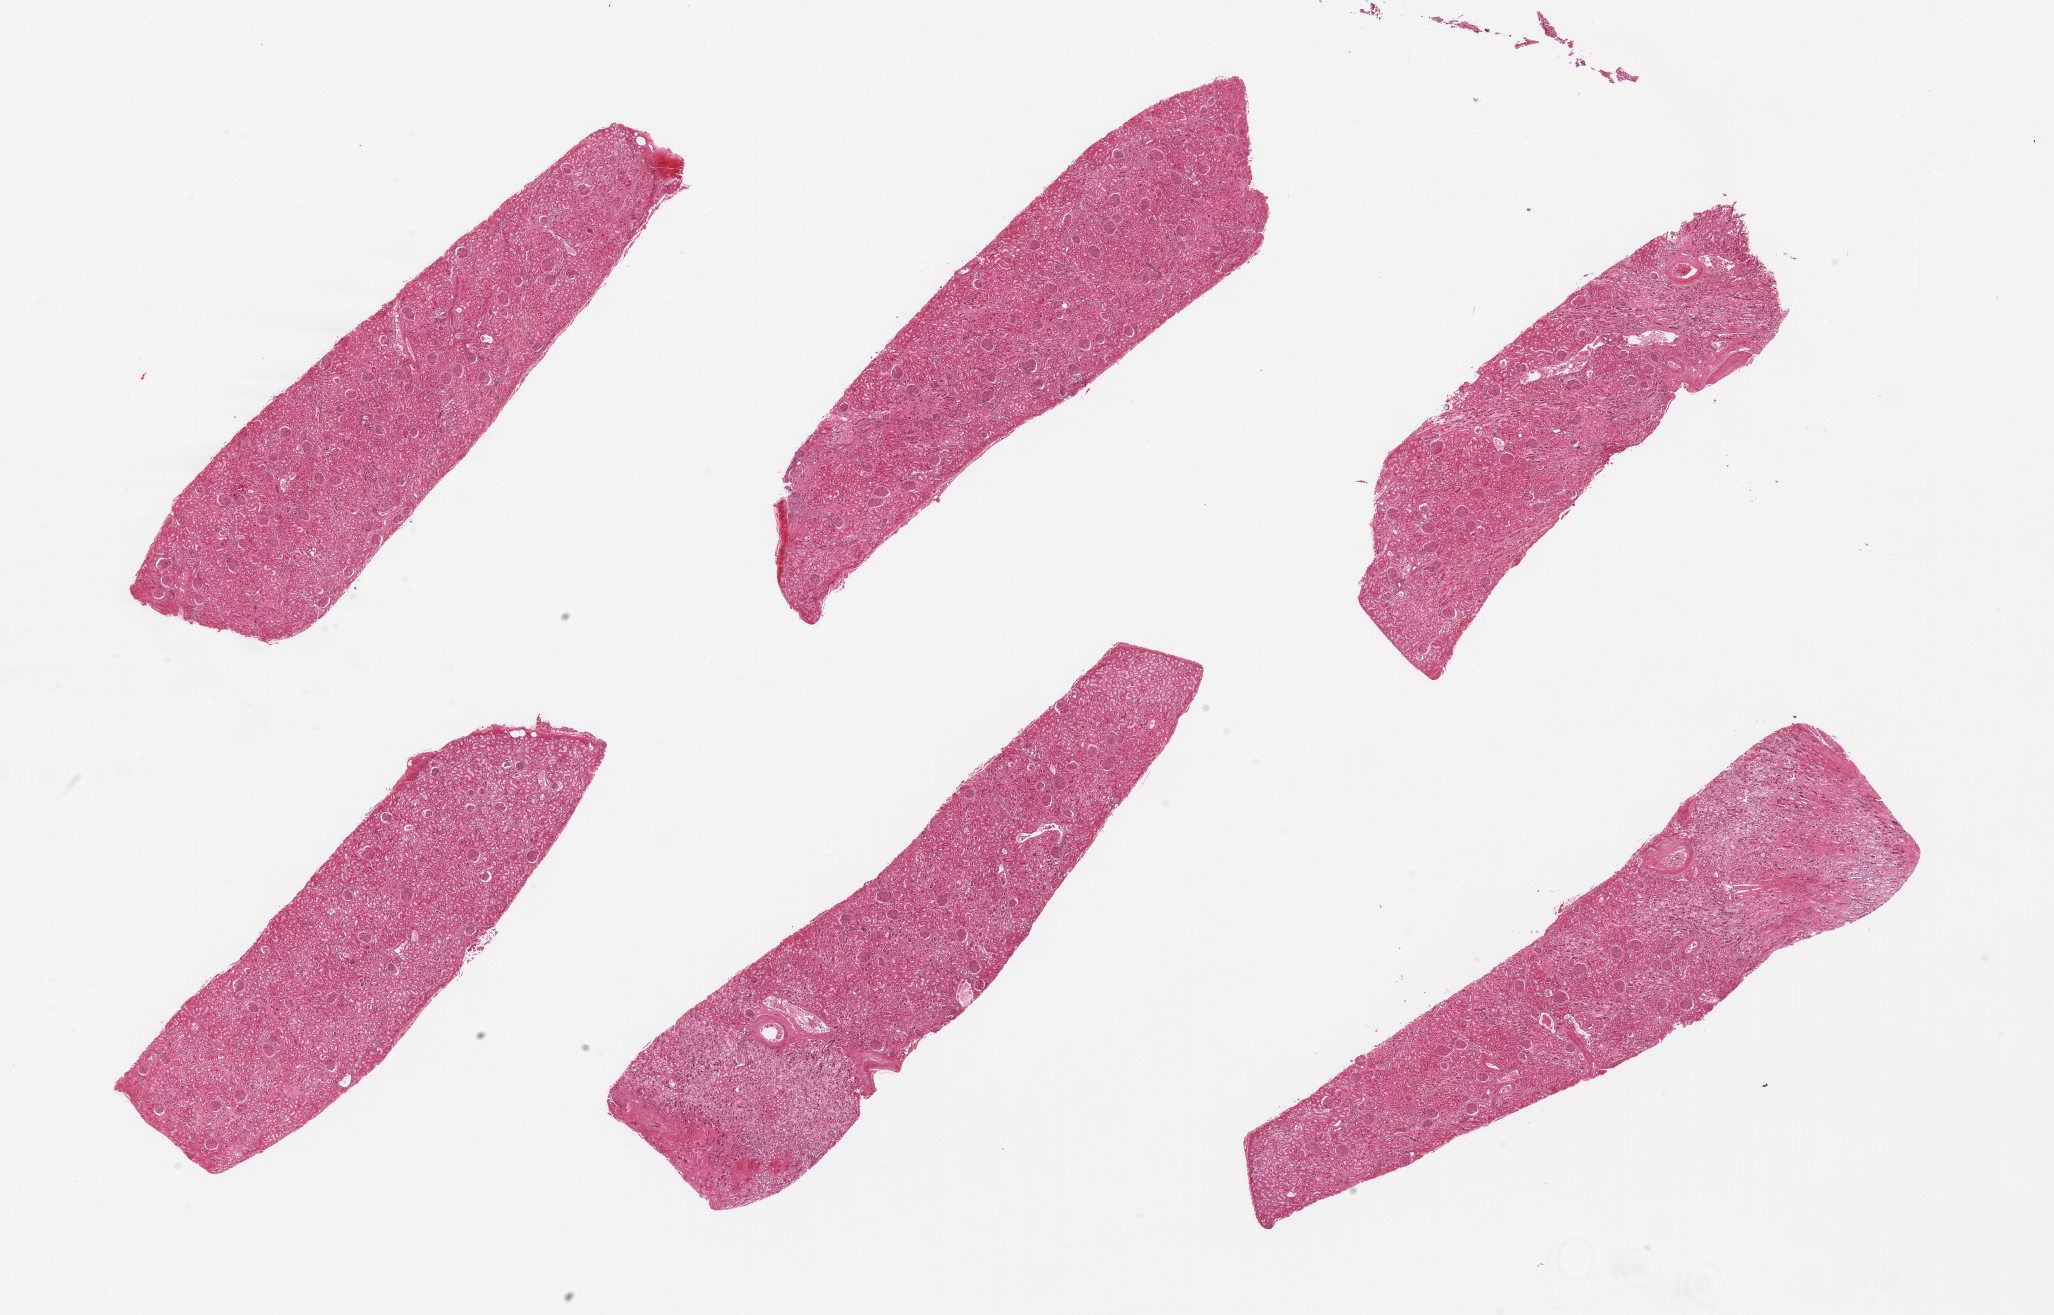
Haematoxylin and eosin whole-slide image — whole scanned area (about 32.5 x 20.8 mm, acquisition: 20x scan) shown as a low-resolution overview. PAXgene-fixed, paraffin-embedded tissue. Sampled site (target tissue): renal cortex. Tissue donor sample.
Reviewer comment on this tissue sample: 6 pieces, includes portion of medulla.